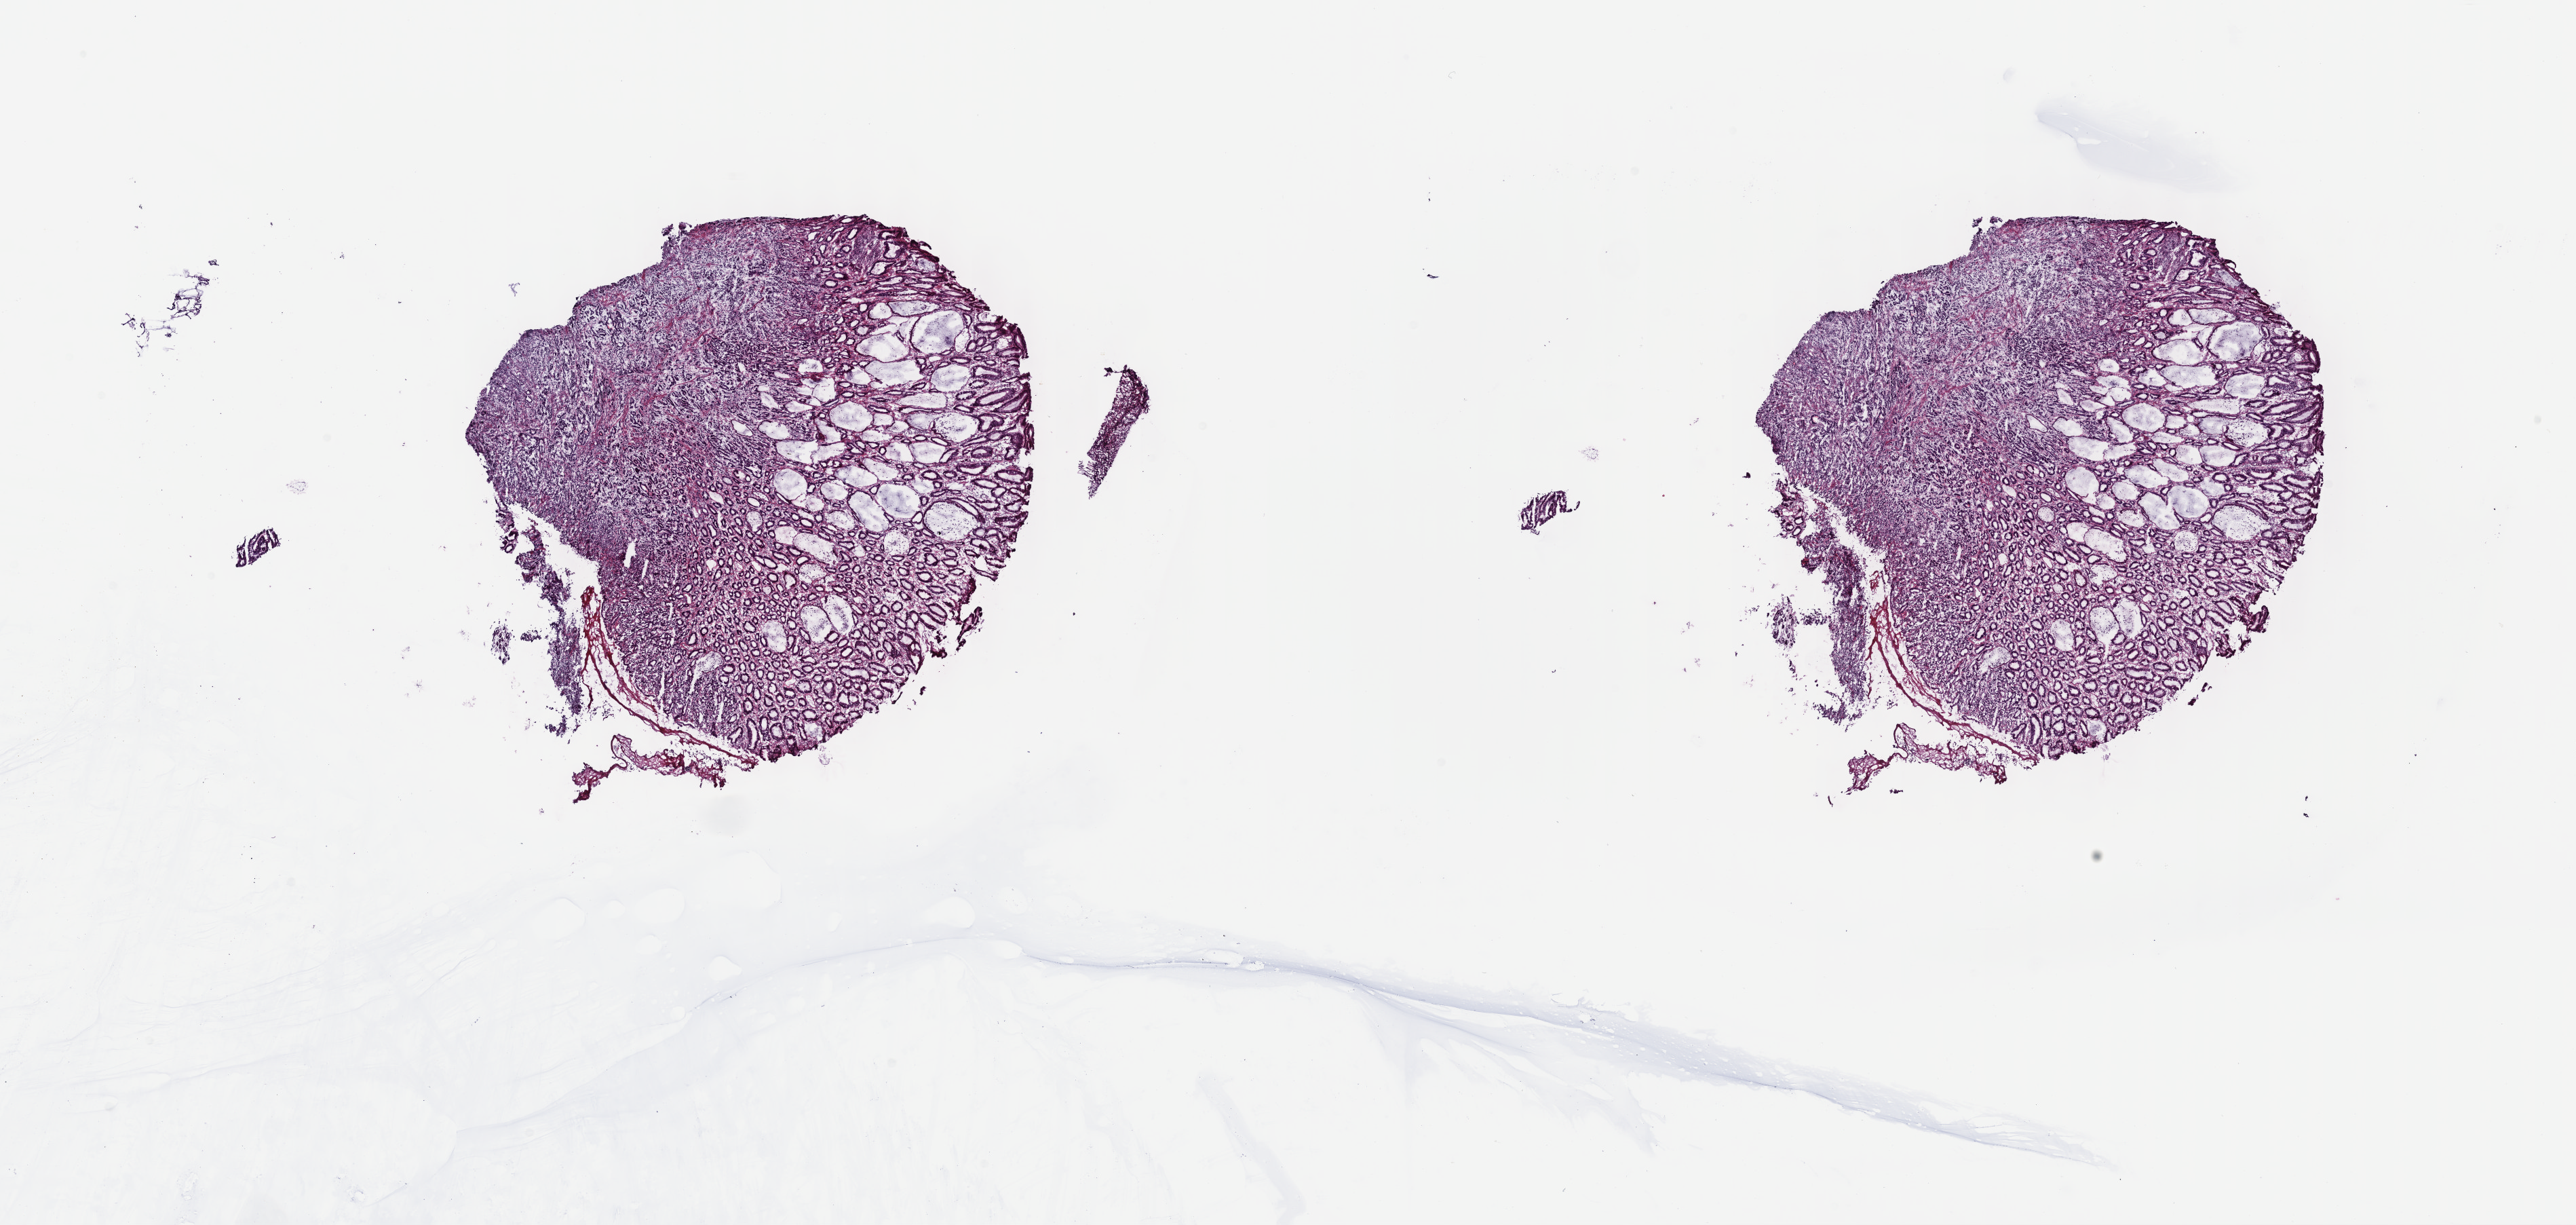
H&E-stained whole-slide image, shown as a low-resolution overview of the whole scanned area (about 30.7 x 14.6 mm). Frozen section from the top of the tissue portion. Stomach, primary tumour sample. Male, age 43 years at initial diagnosis. Histologic grade: G3 (poorly differentiated). Pathologist review of this section (percent, as recorded): tumour cells 70%, tumour nuclei 70%, normal cells 10%, stromal cells 20%, necrosis 0%. Infiltration values recorded for this section: lymphocyte infiltration 40%, monocyte infiltration 20%, neutrophil infiltration 20%.
AJCC pathologic stage: IIIB (7th edition). Pathologic diagnosis: Adenocarcinoma, intestinal type (body of stomach). Lymph nodes positive (case pathology): 9 of 53 examined.